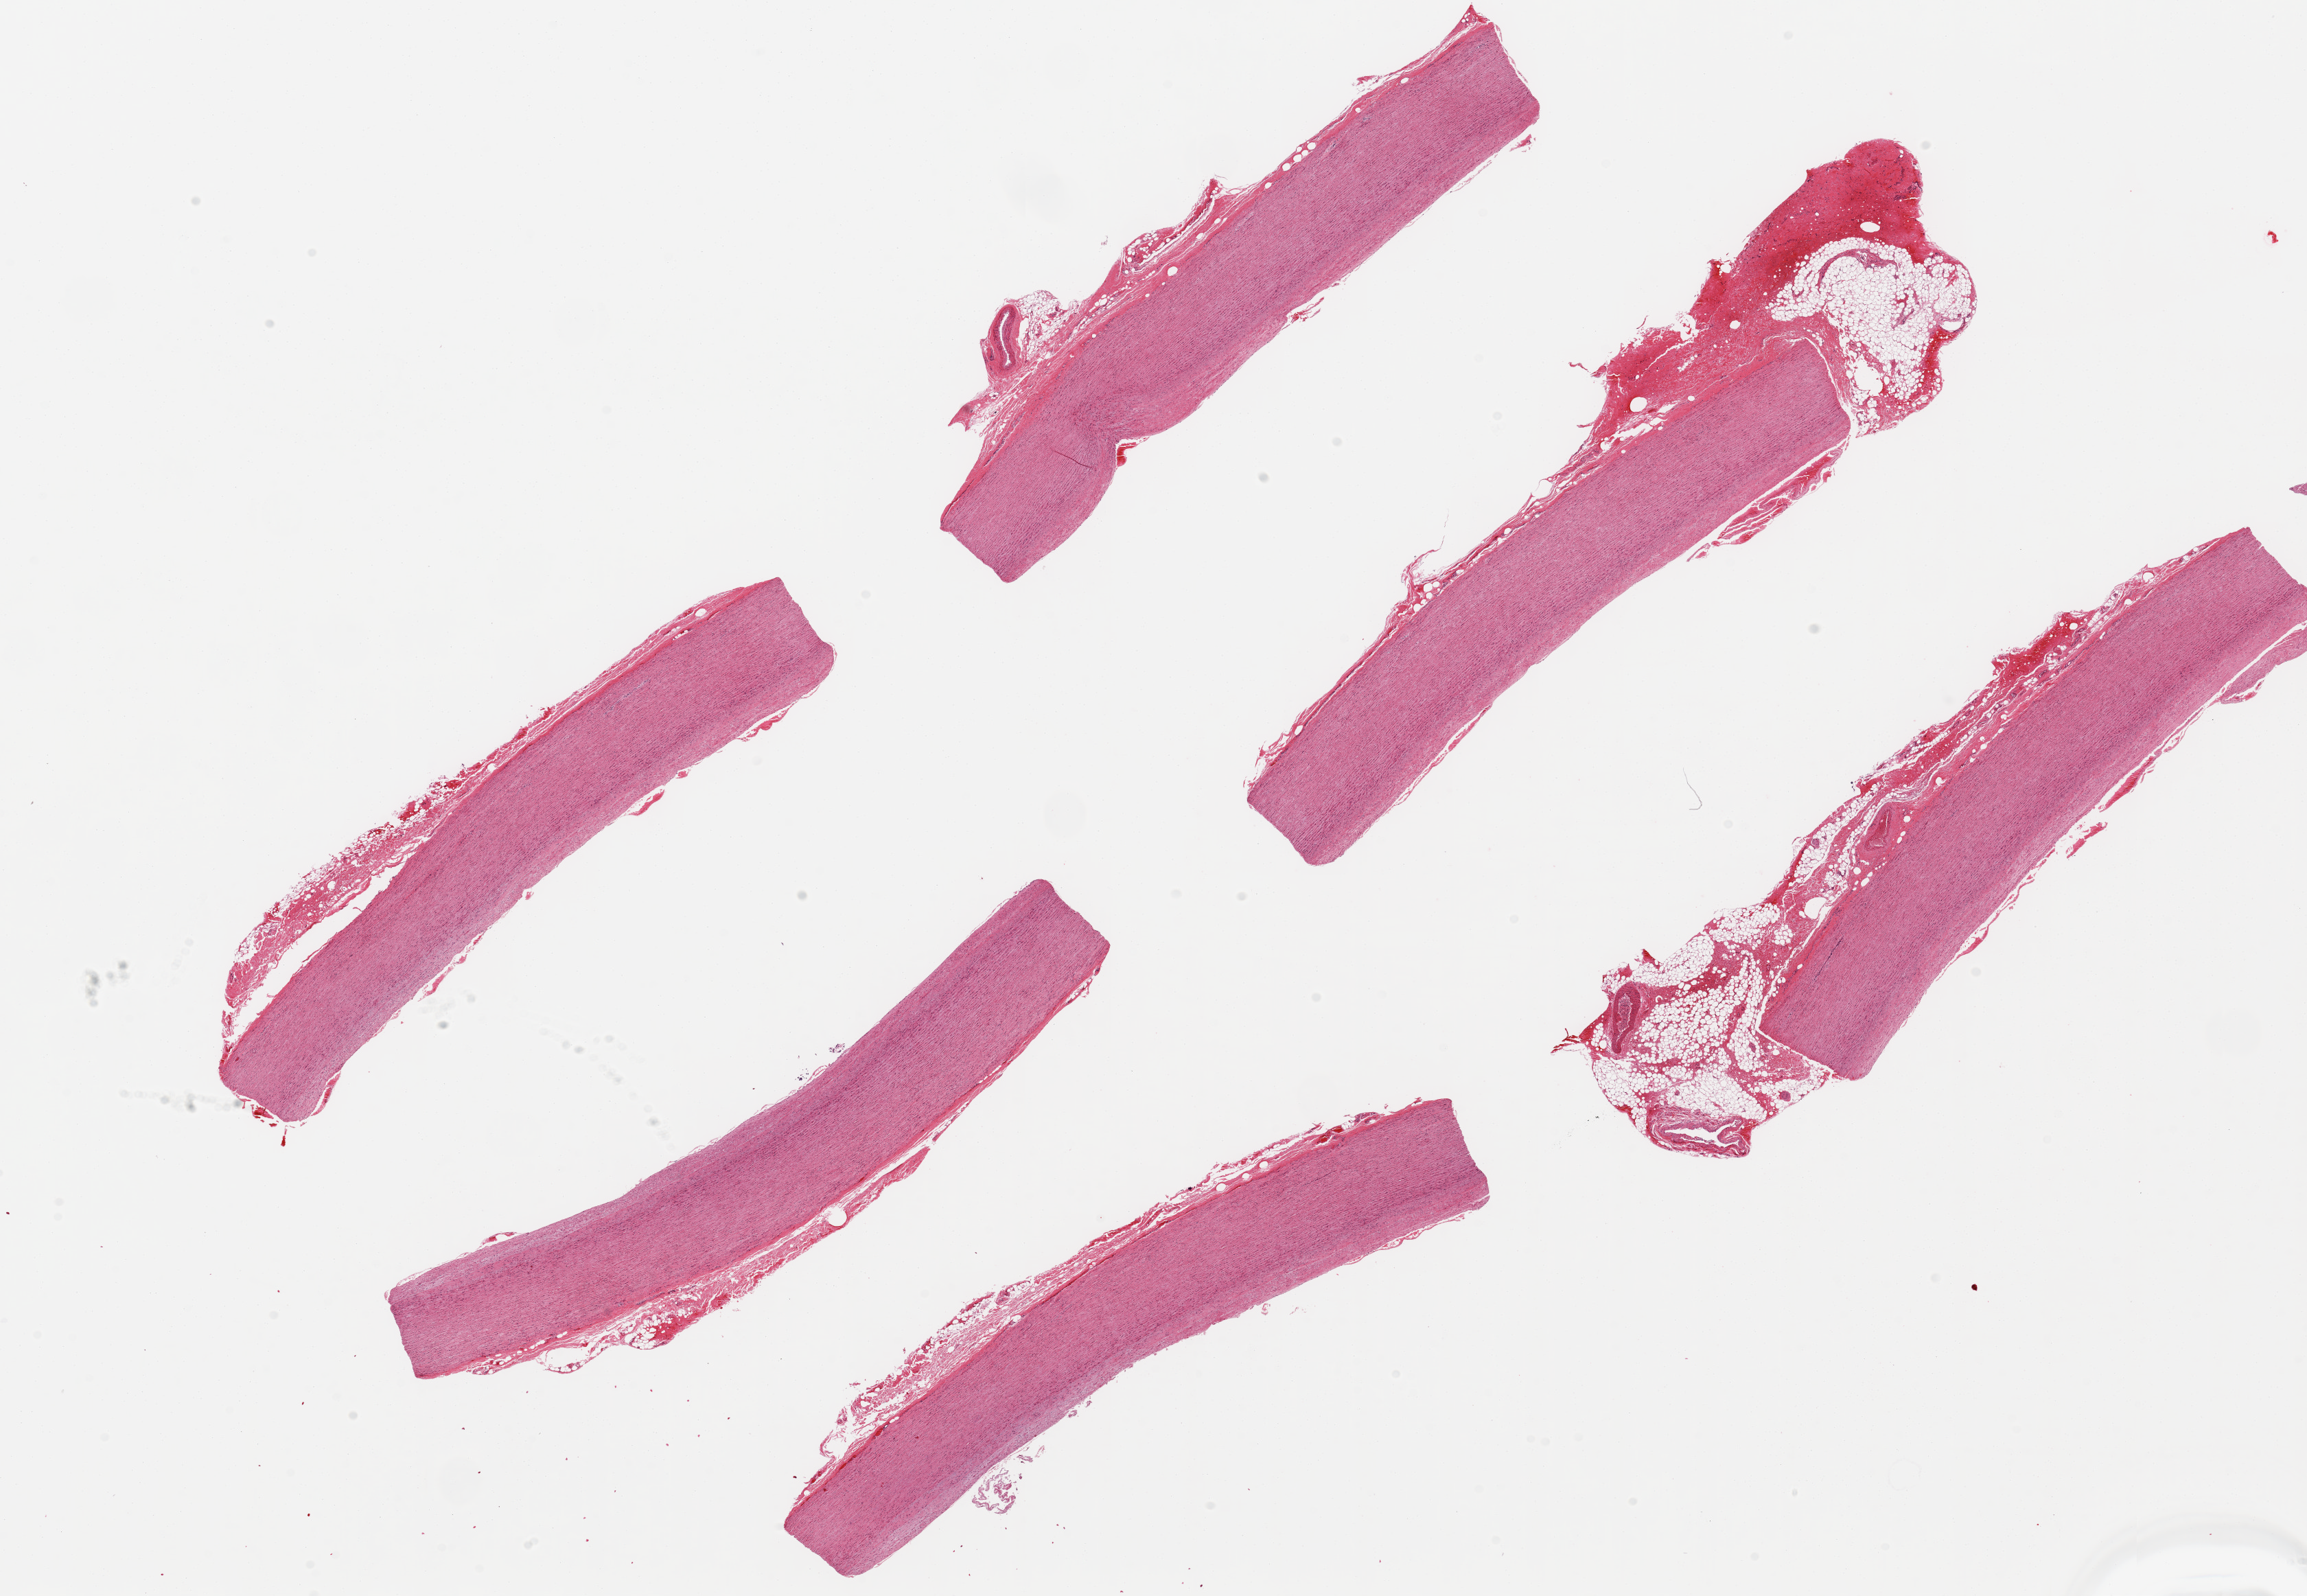
Whole-slide image, H&E stain, a low-resolution overview of the entire scanned area, about 26.6 x 18.4 mm (from a 20x scan). PAXgene-fixed, paraffin-embedded tissue. Target tissue: aorta. Tissue donor sample. Donor: male.
Reviewer comment on this tissue sample: 6 ~8.5x1.5mm pieces, several with adherent fat/fibrous tissue up to ~5.2mm.